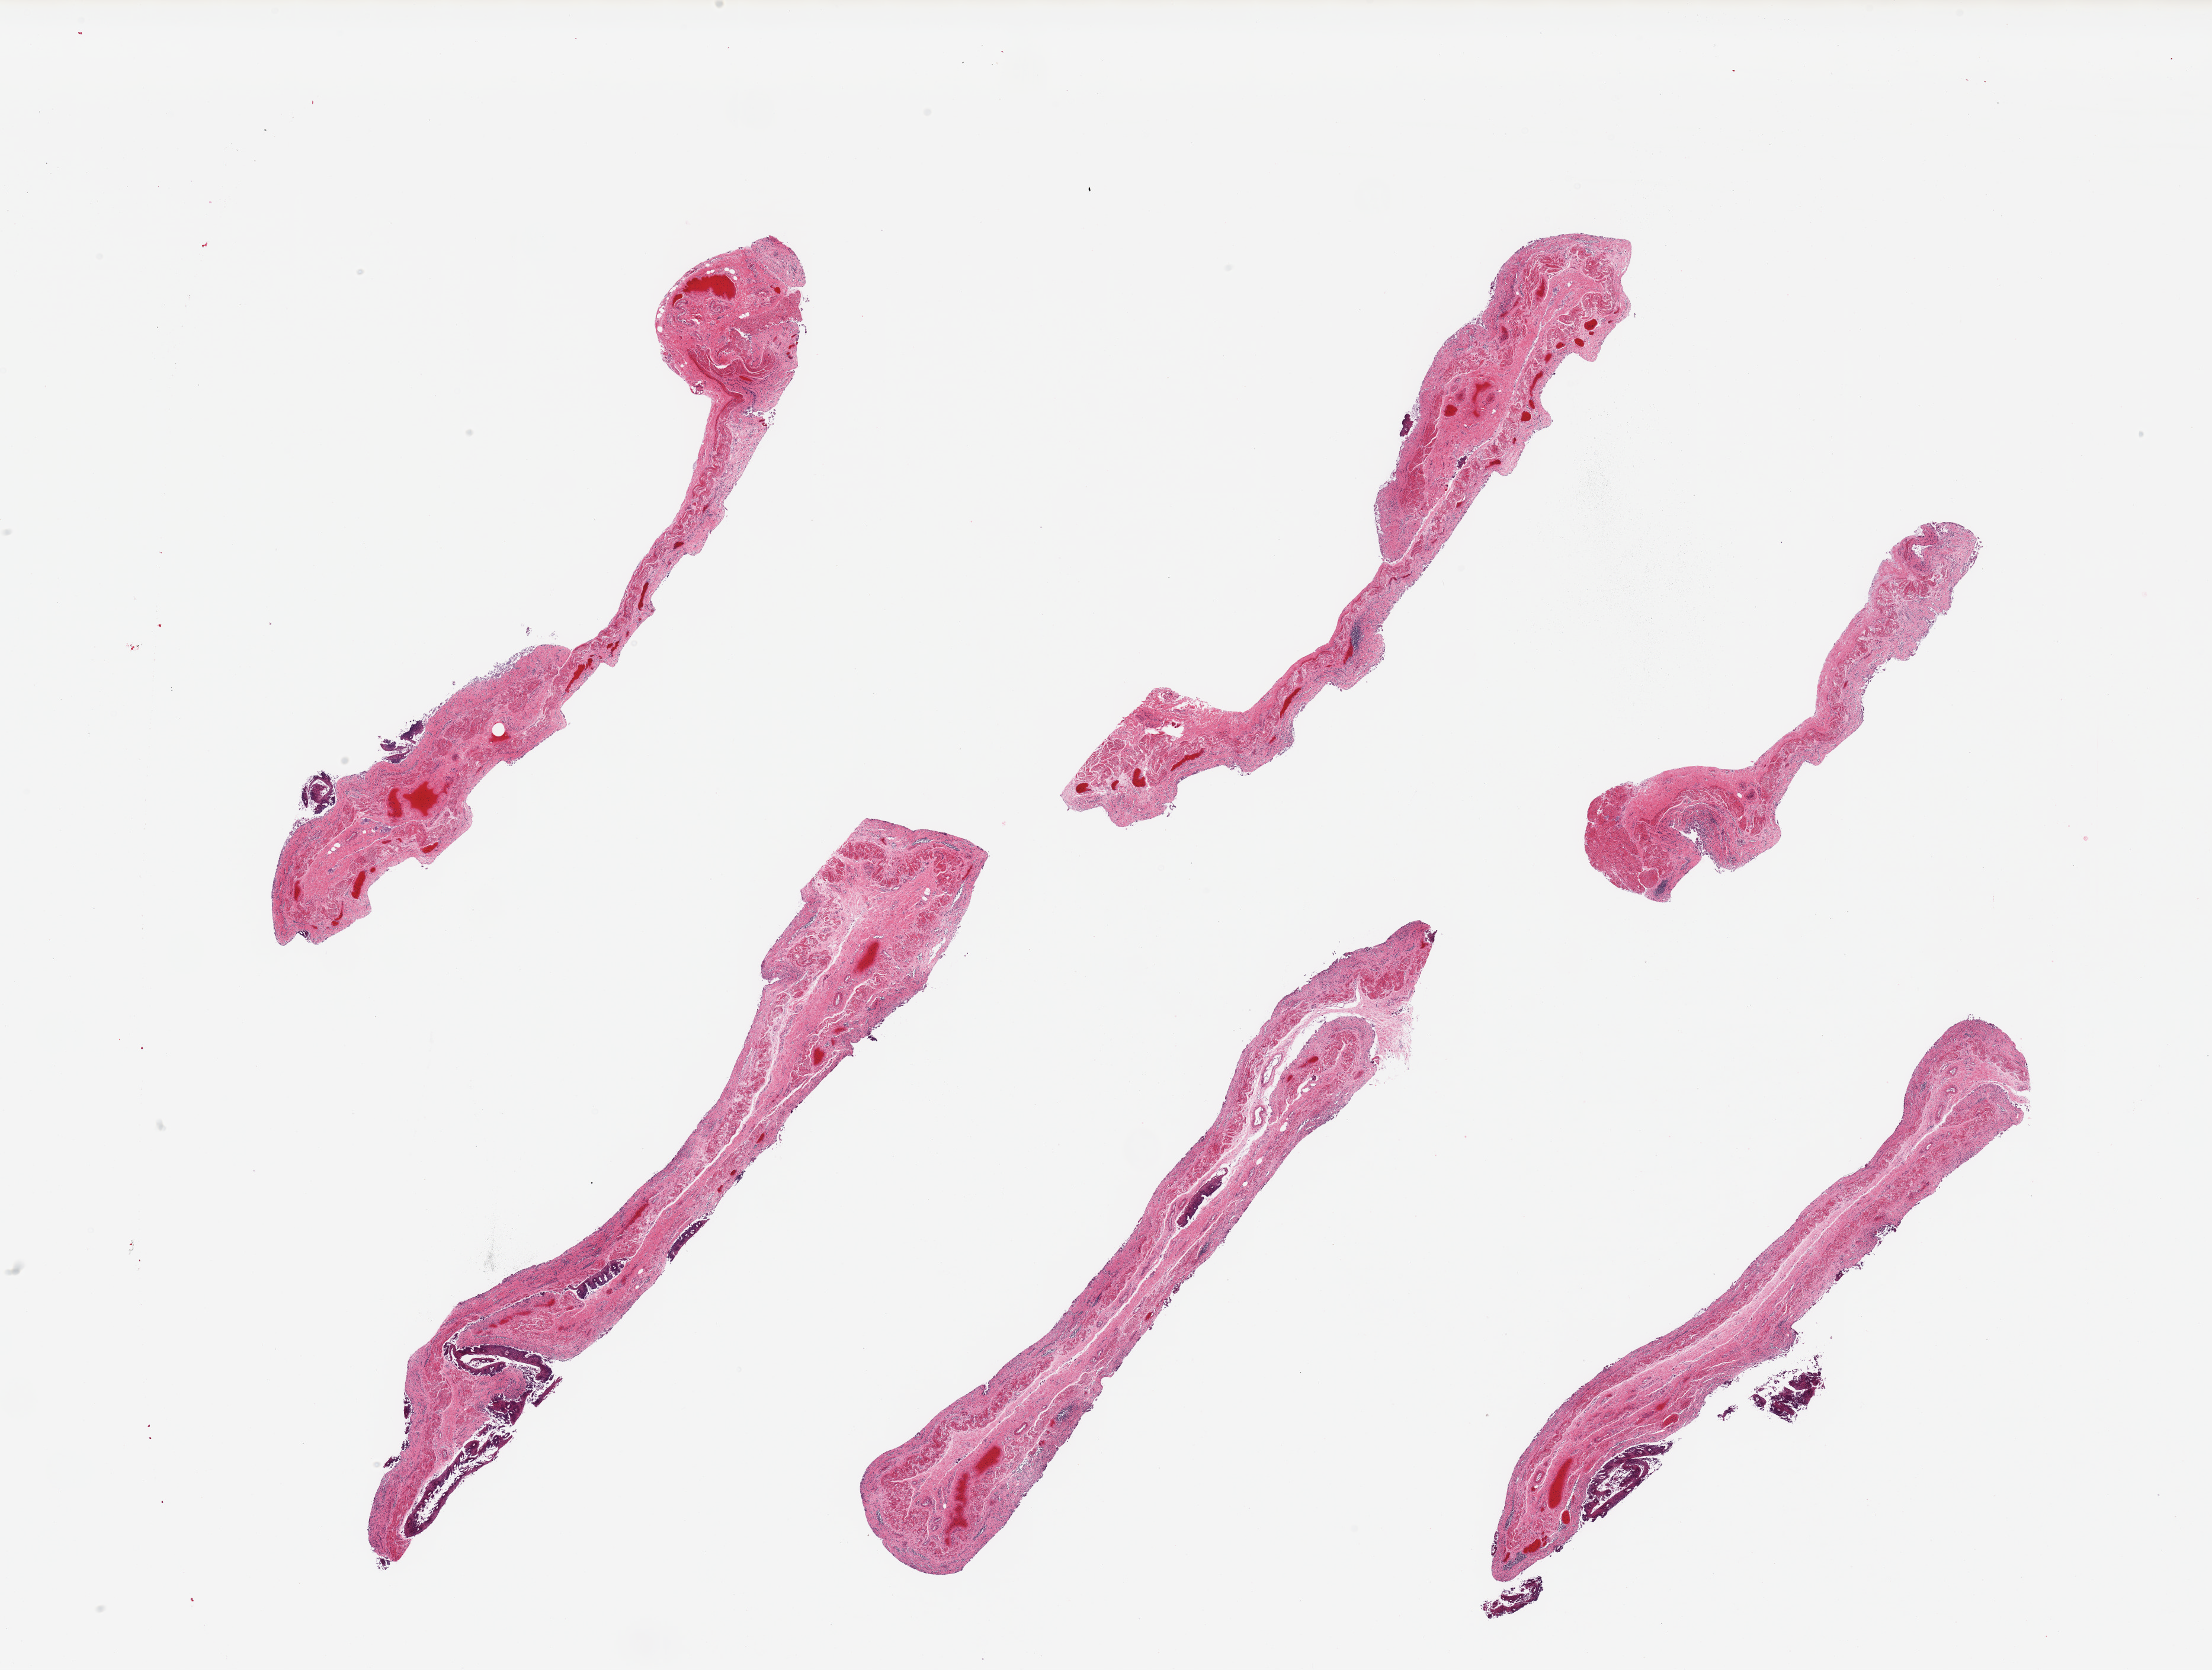
Whole-slide image, H&E stain, low-resolution overview of the scanned area, about 29.5 x 22.3 mm, PAXgene-fixed, paraffin-embedded tissue, target tissue: esophageal mucous membrane, tissue donor sample. Donor: male.
Review note (as recorded): 6 pieces; 90% squamous epithelium sloughed.